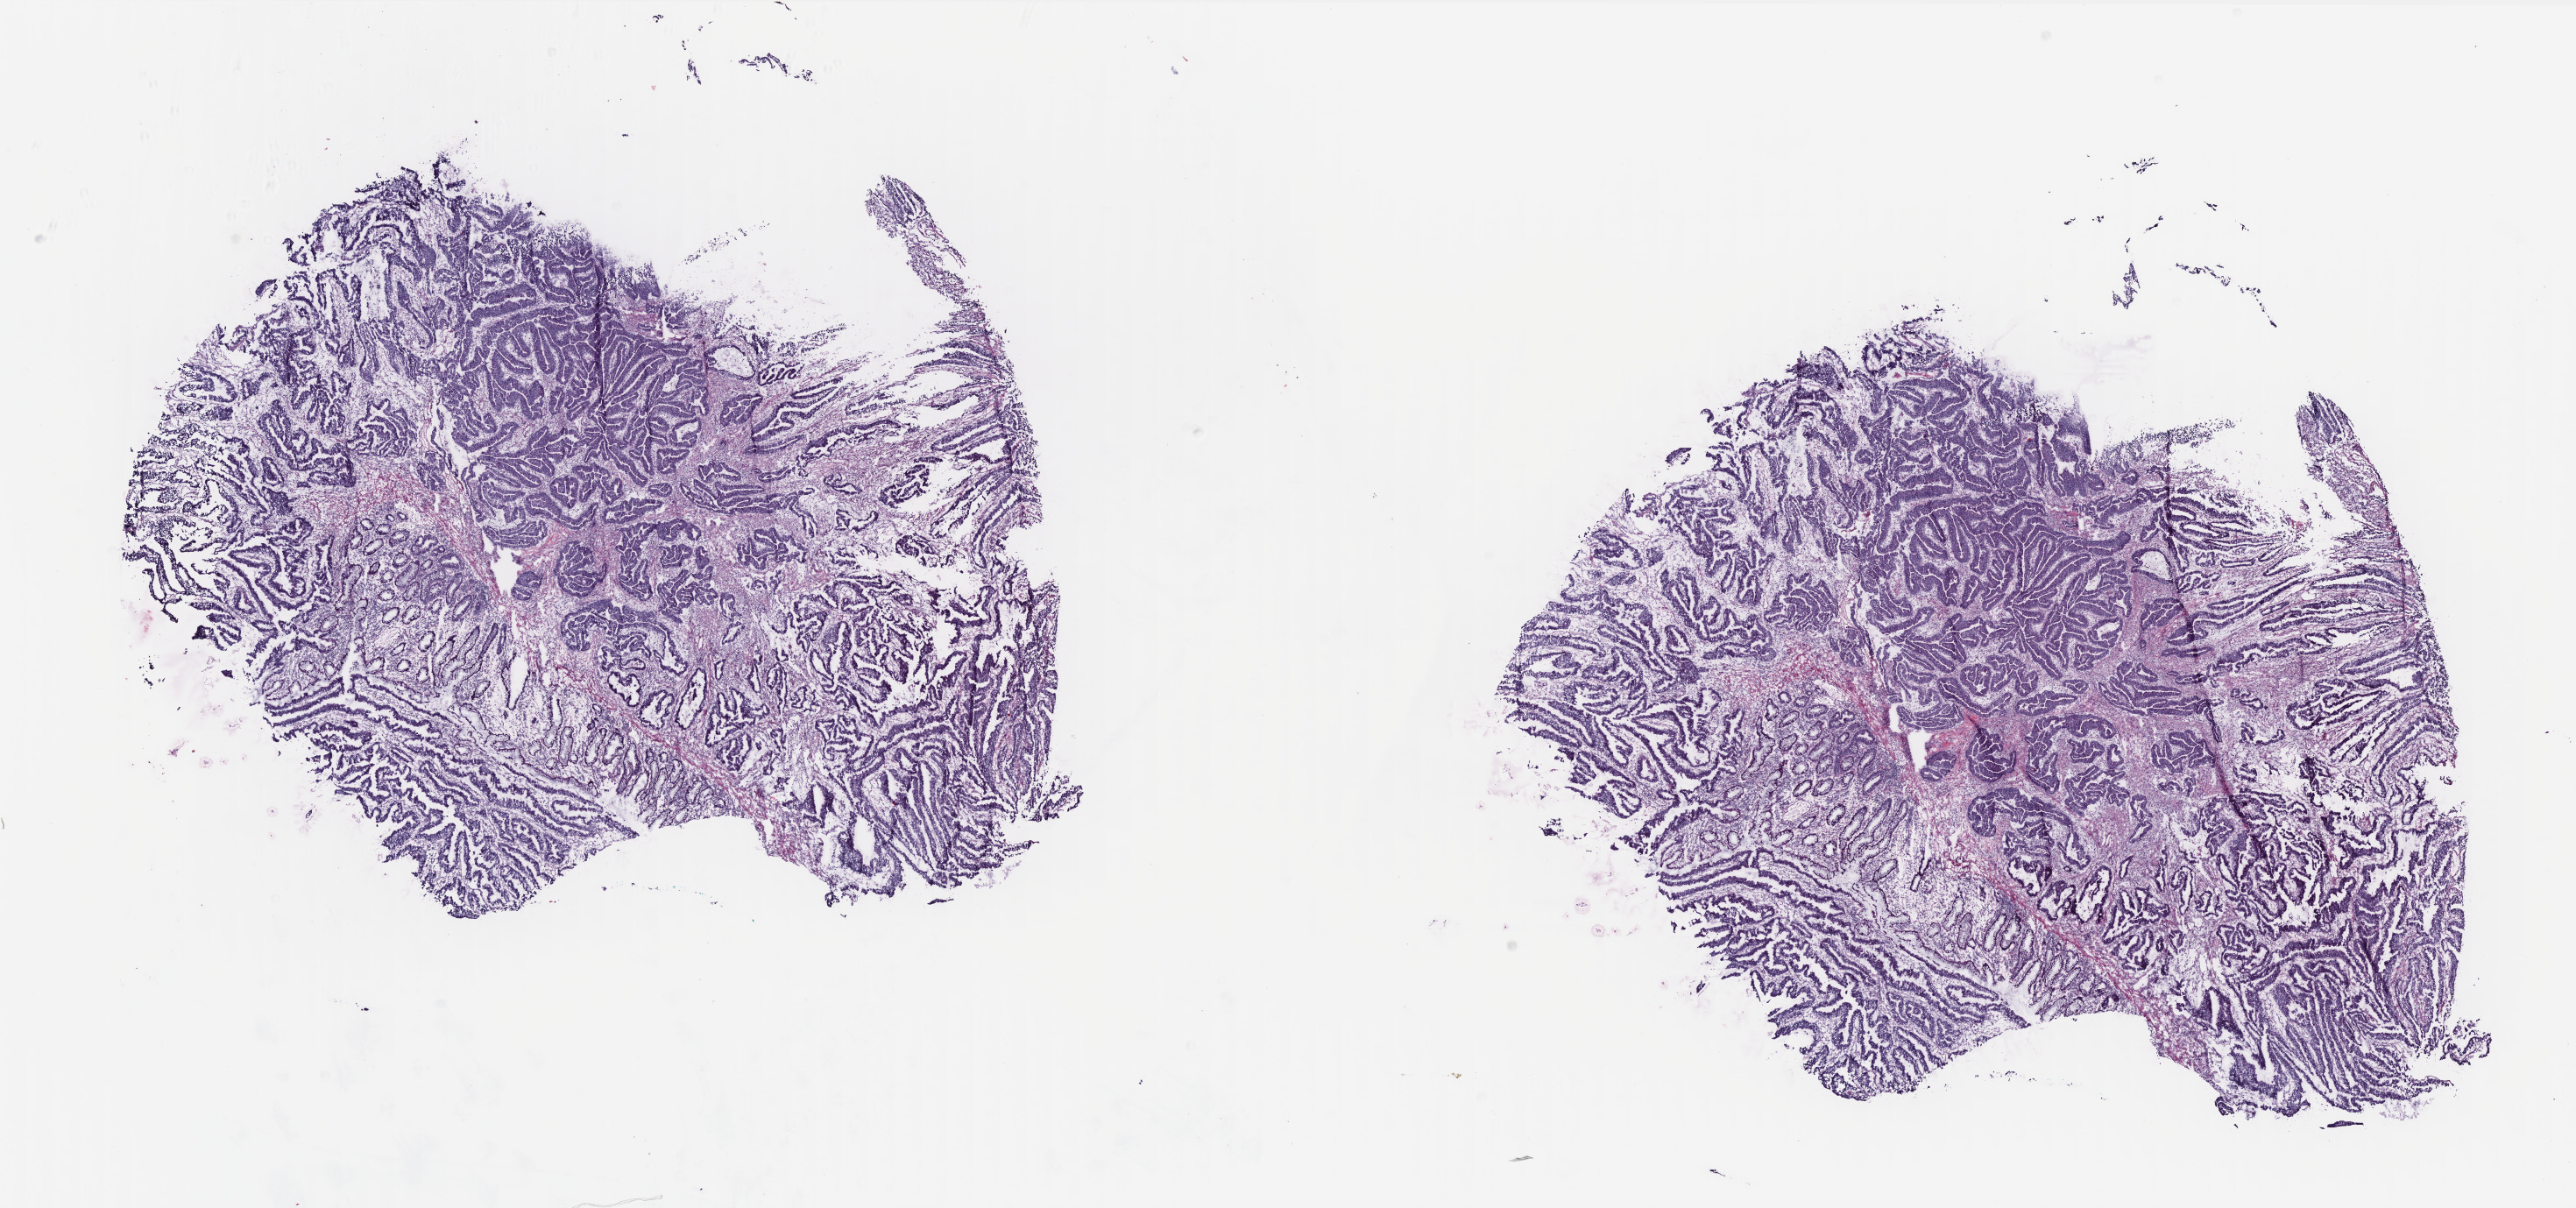
Digitized H&E-stained tissue section (whole slide) — a low-resolution overview of the entire scanned area, about 23.6 x 11.1 mm, frozen section, primary tumour sample from the rectum. Male patient; age at initial diagnosis 77 years. Pathologist review of this section (percent, as recorded): tumour cells 59%, tumour nuclei 60%, normal cells 15%, stromal cells 25%, necrosis 1%. Inflammatory infiltration, as recorded: lymphocyte infiltration 15%, monocyte infiltration 1%, neutrophil infiltration 1%.
* AJCC pathologic stage: I
* histologic diagnosis: Adenocarcinoma, NOS